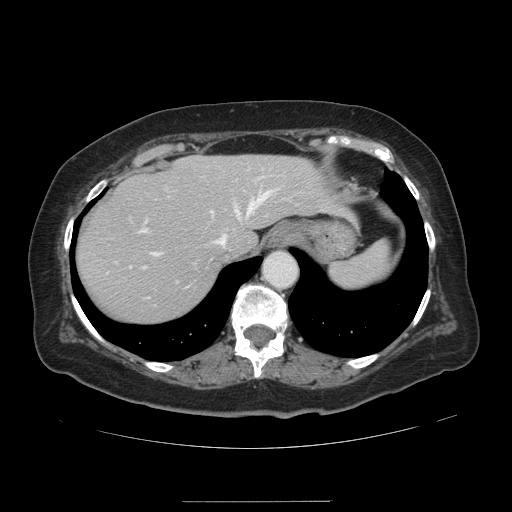
Contrast-enhanced abdominal CT, one axial slice. Position 108 of 141 along the scan axis. 120 kVp. Intravenous contrast given. Soft-tissue window (W 400 / L 40 HU). 2.5 mm slice thickness. 512 × 512 image matrix, field of view 393 × 393 mm. Female patient, age 74 years. From the clinical record (not read from this slice): diagnosis: colorectal cancer liver metastases, imaged before liver resection; multiple liver metastases: yes; largest metastasis: 7 cm.
Structures marked on this image (expert manual segmentation):
- hepatic veins: bounding box <150,192,269,257> (left, top, right, bottom; pixels)
- liver: <76,155,342,322>
- planned liver remnant (the part of the liver to remain after resection): <76,155,342,322>
- portal vein (with intrahepatic branches): <129,192,263,267>